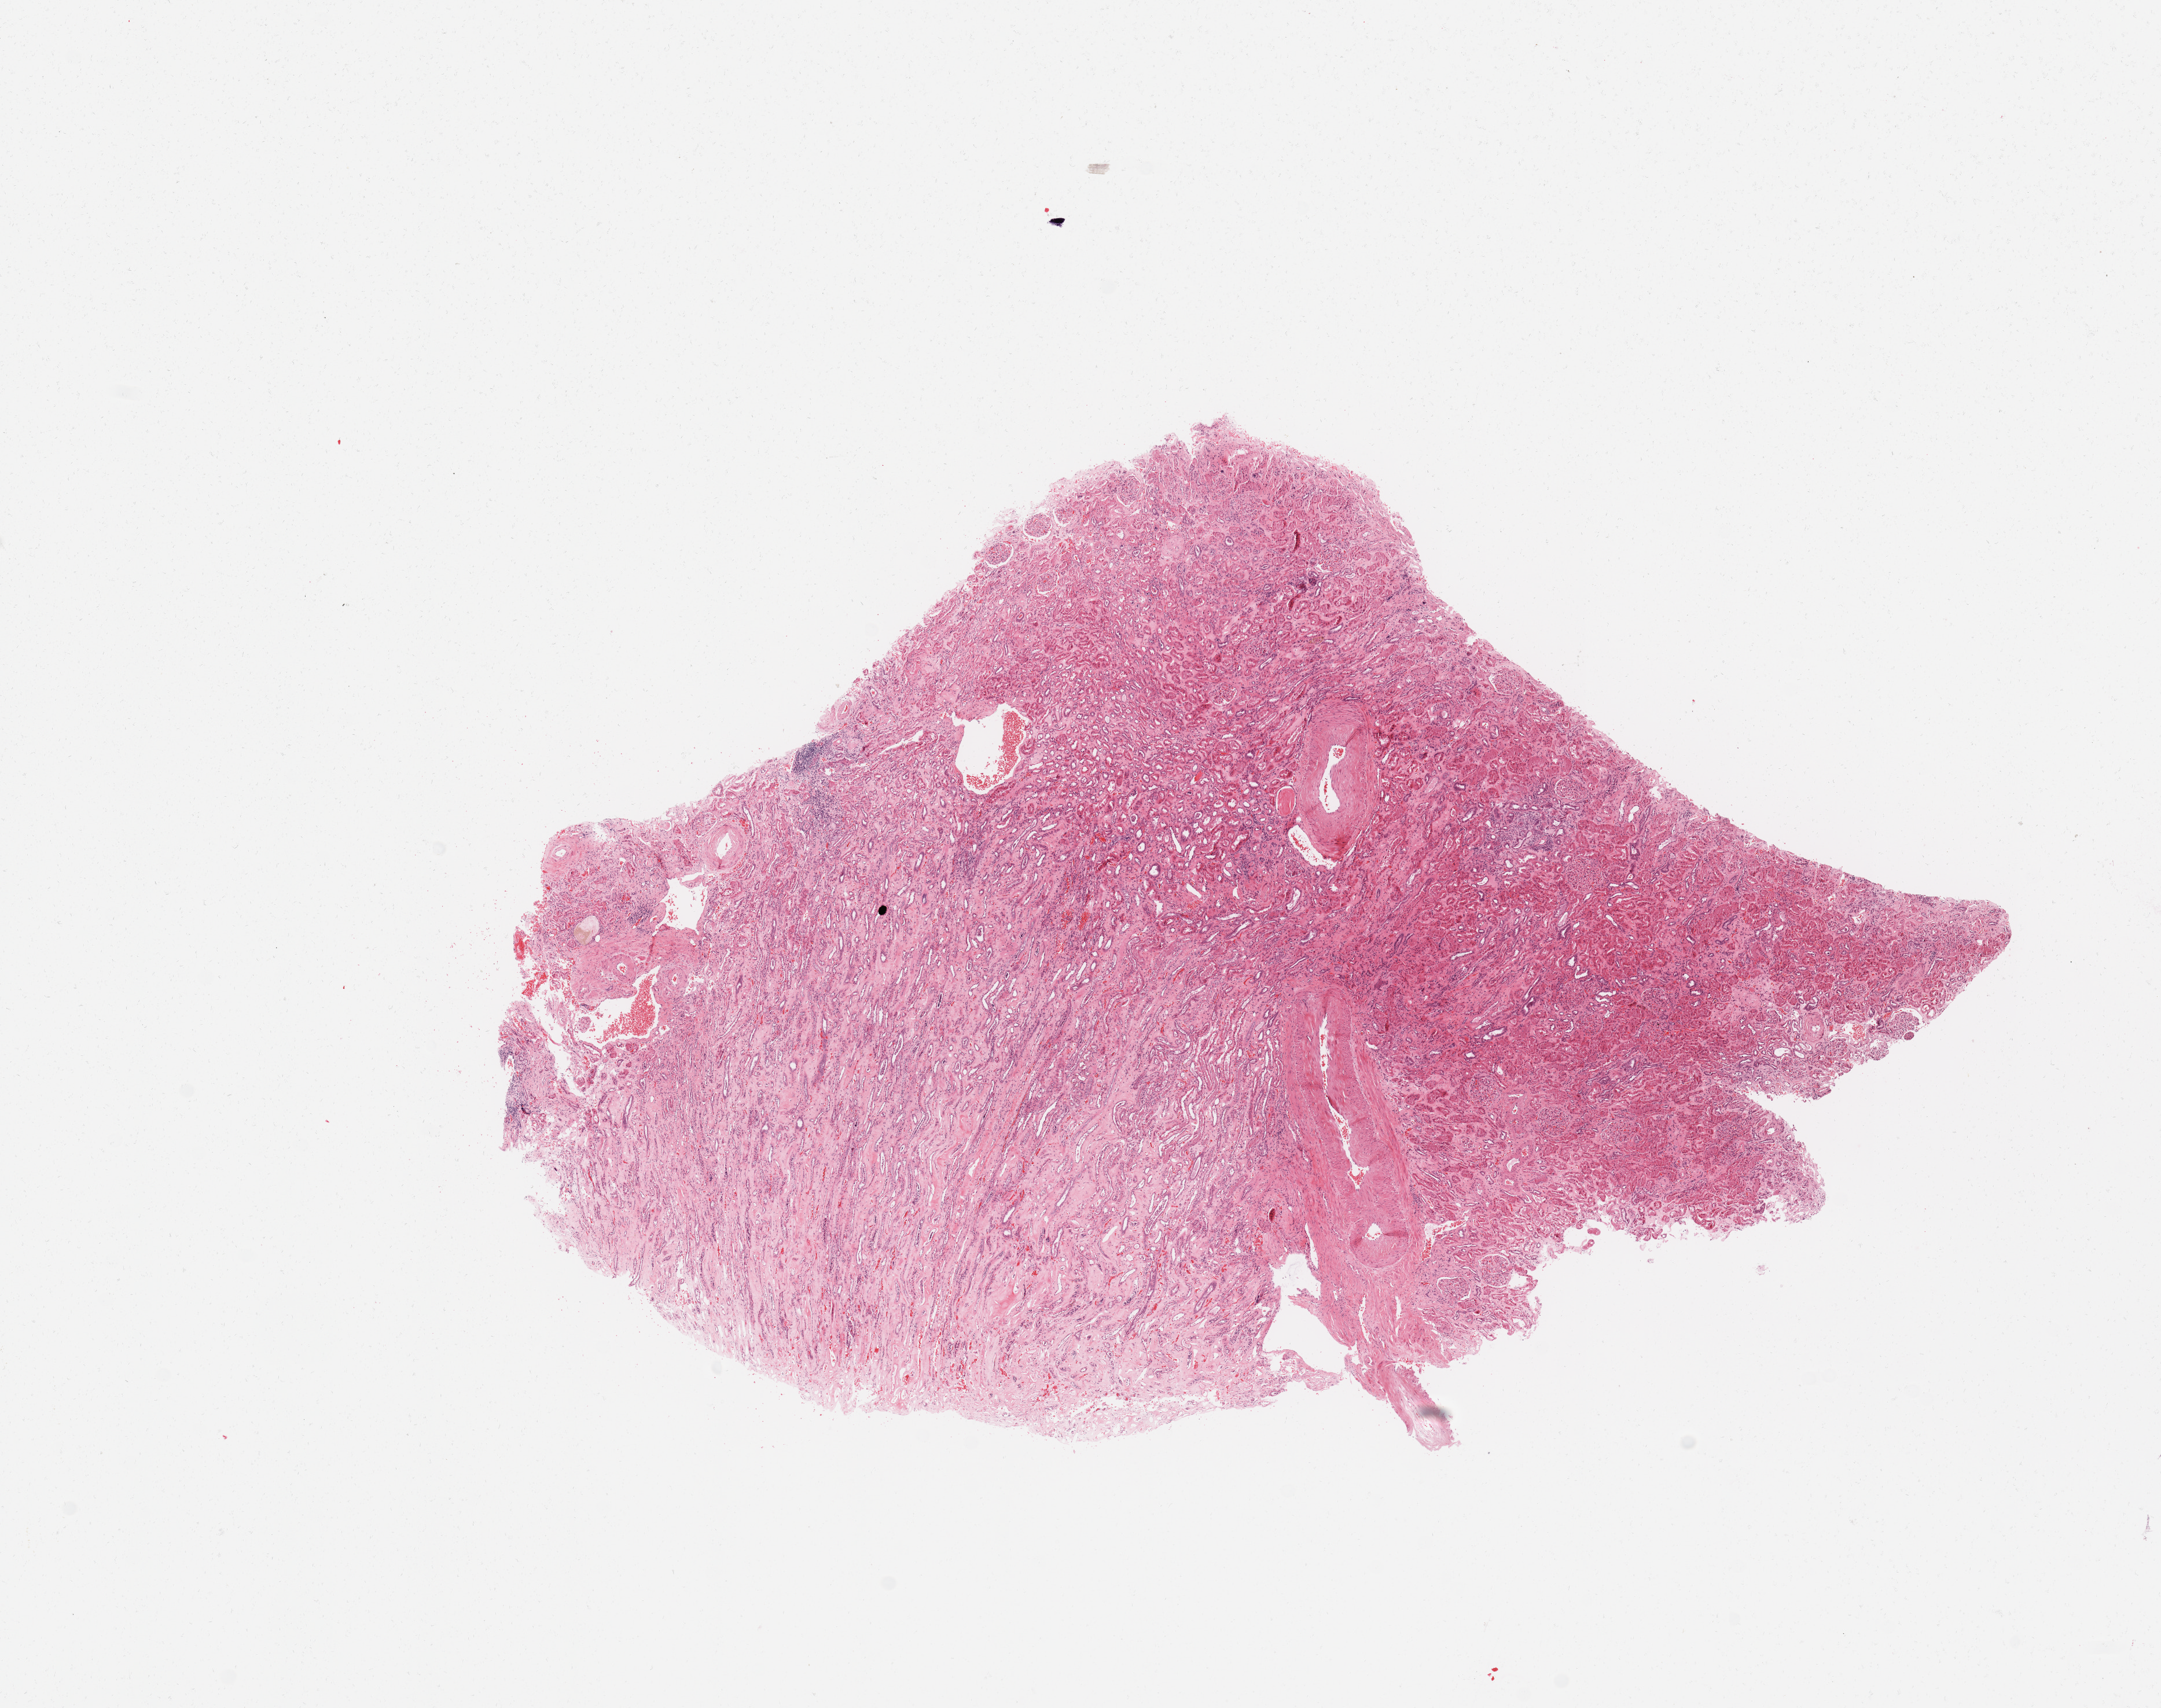
Whole-slide histology image, Hematoxylin and eosin (H&E) stained — shown as a low-resolution overview of the whole scanned area (about 14.8 x 11.7 mm, acquisition: 20x scan); kidney, normal (non-tumour) tissue. Male, 76 y/o.
• this section: normal (non-tumour) tissue from the same patient
• patient diagnosis: Renal cell carcinoma, NOS